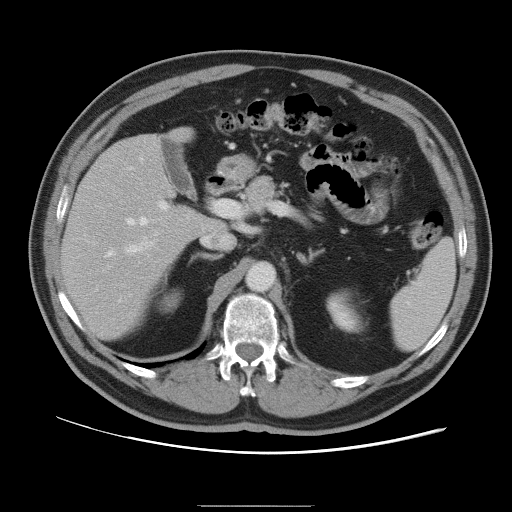
Contrast-enhanced abdominal CT, one axial slice. Slice 57 of 105 in the series (ordered by position). Soft-tissue window (W 400 / L 40 HU). 512 × 512 image matrix, field of view 399 × 399 mm. Male patient, age 64 years. From the clinical record (not read from this slice): diagnosis: colorectal cancer liver metastases, imaged before liver resection; multiple liver metastases: yes.
Annotated regions visible in this slice (manually delineated by an expert):
- hepatic veins: bounding box <107,167,148,256> (left, top, right, bottom; pixels)
- liver: <63,136,215,340>
- planned liver remnant (the part of the liver to remain after resection): <63,136,216,340>
- portal vein (with intrahepatic branches): <125,201,169,297>